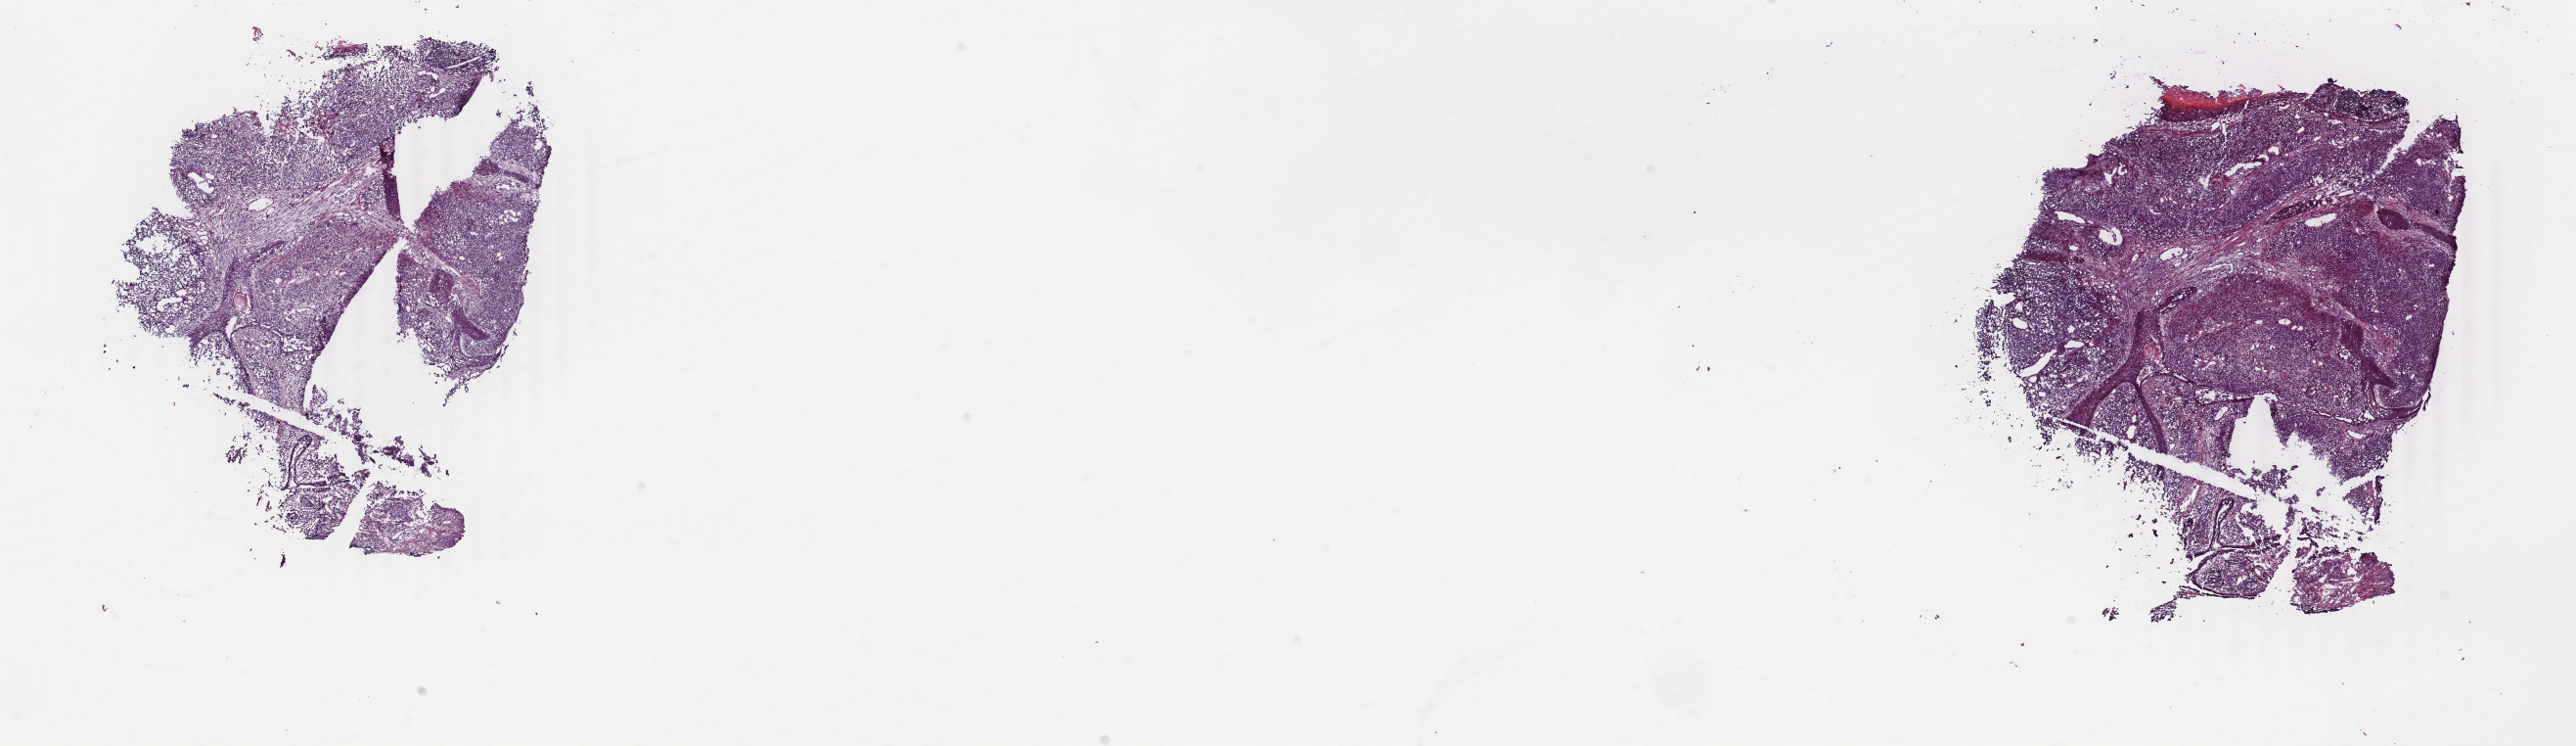
Hematoxylin and eosin (H&E) stained whole-slide image — shown as a low-resolution overview of the whole scanned area (about 20.9 x 6.1 mm). Frozen section. Primary tumour sample from the skin. Patient: female, age at initial diagnosis 75 years. Slide review estimates, as recorded: tumour cells 80%, tumour nuclei 65%, normal cells 20%, stromal cells 0%, necrosis 0%. Inflammatory infiltration, as recorded: lymphocyte infiltration 0%, monocyte infiltration 0%, neutrophil infiltration 0%.
* histologic diagnosis: Malignant melanoma, NOS
* AJCC pathologic stage: IIC (7th edition)